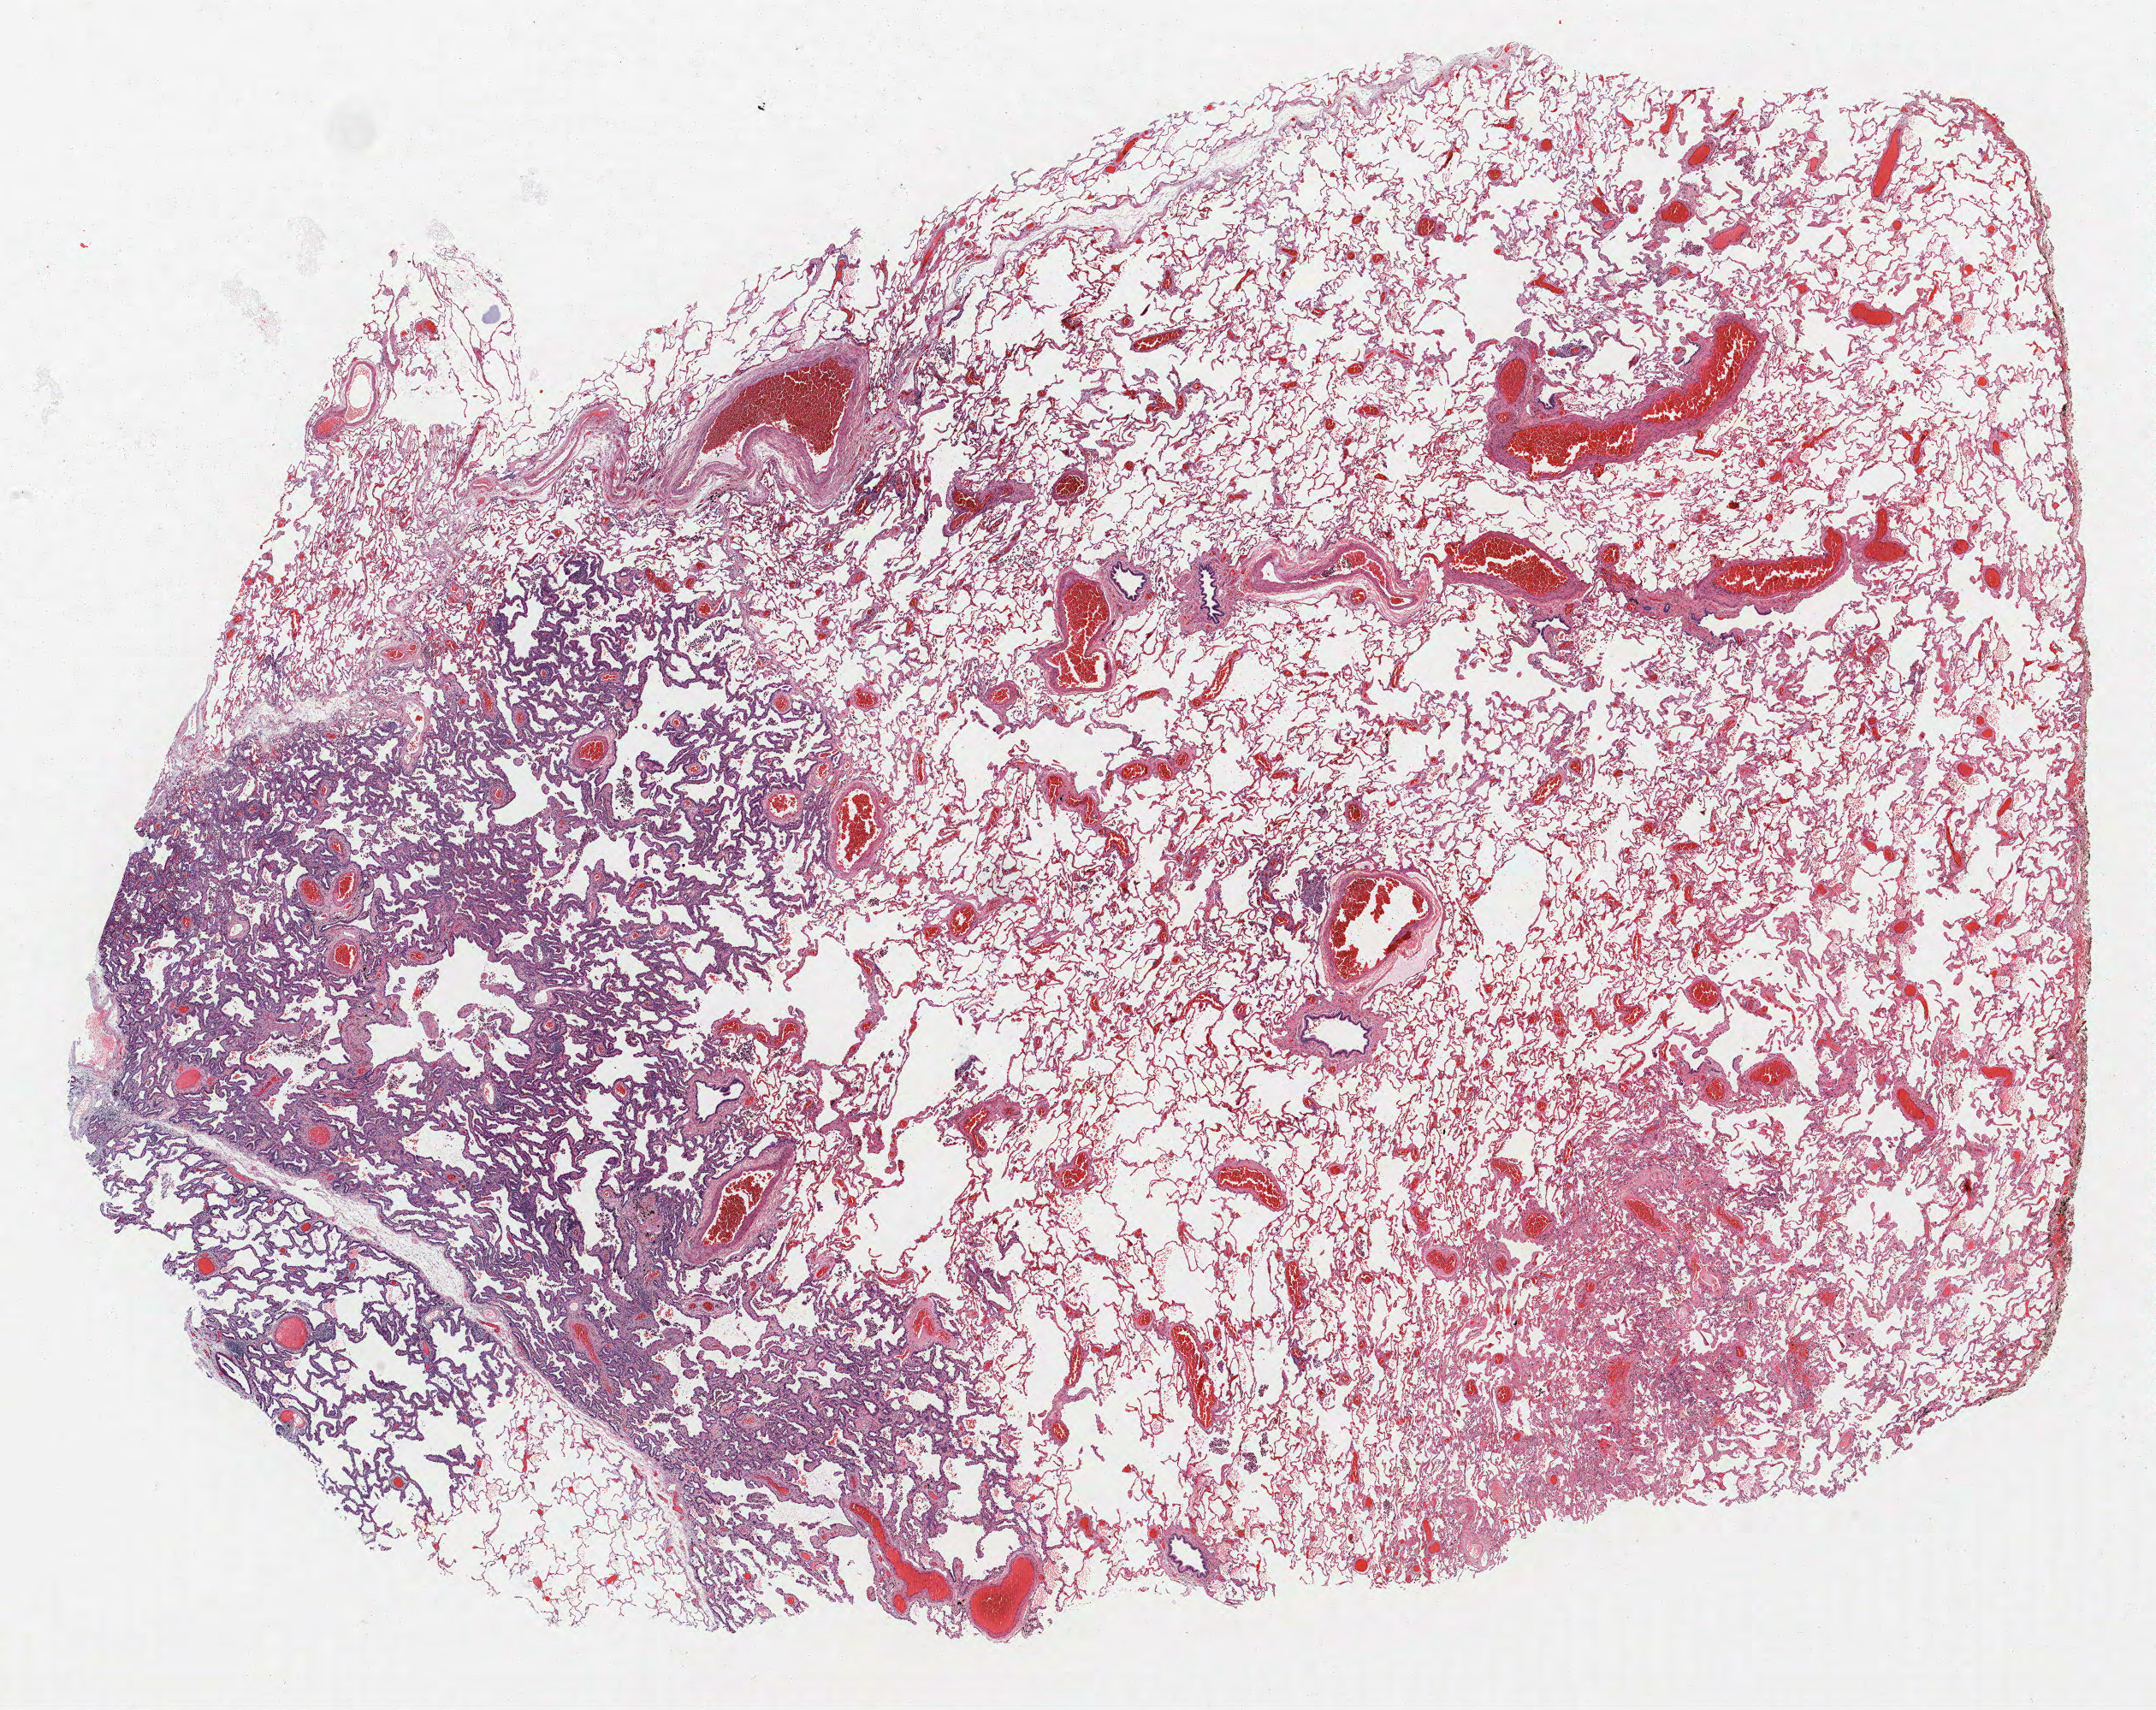
H&E whole-slide image — whole scanned area (about 20.2 x 16.0 mm) shown as a low-resolution overview; FFPE section; lung tissue. Female, age 65 at enrolment. Former smoker at enrolment. Grade: moderately differentiated (G2).
Participant's lung-cancer diagnosis: Adenocarcinoma, NOS. Primary tumour location (clinical record): left upper lobe. Tumour size (pathology): 30 mm. Stage (AJCC 6th edition): IA.